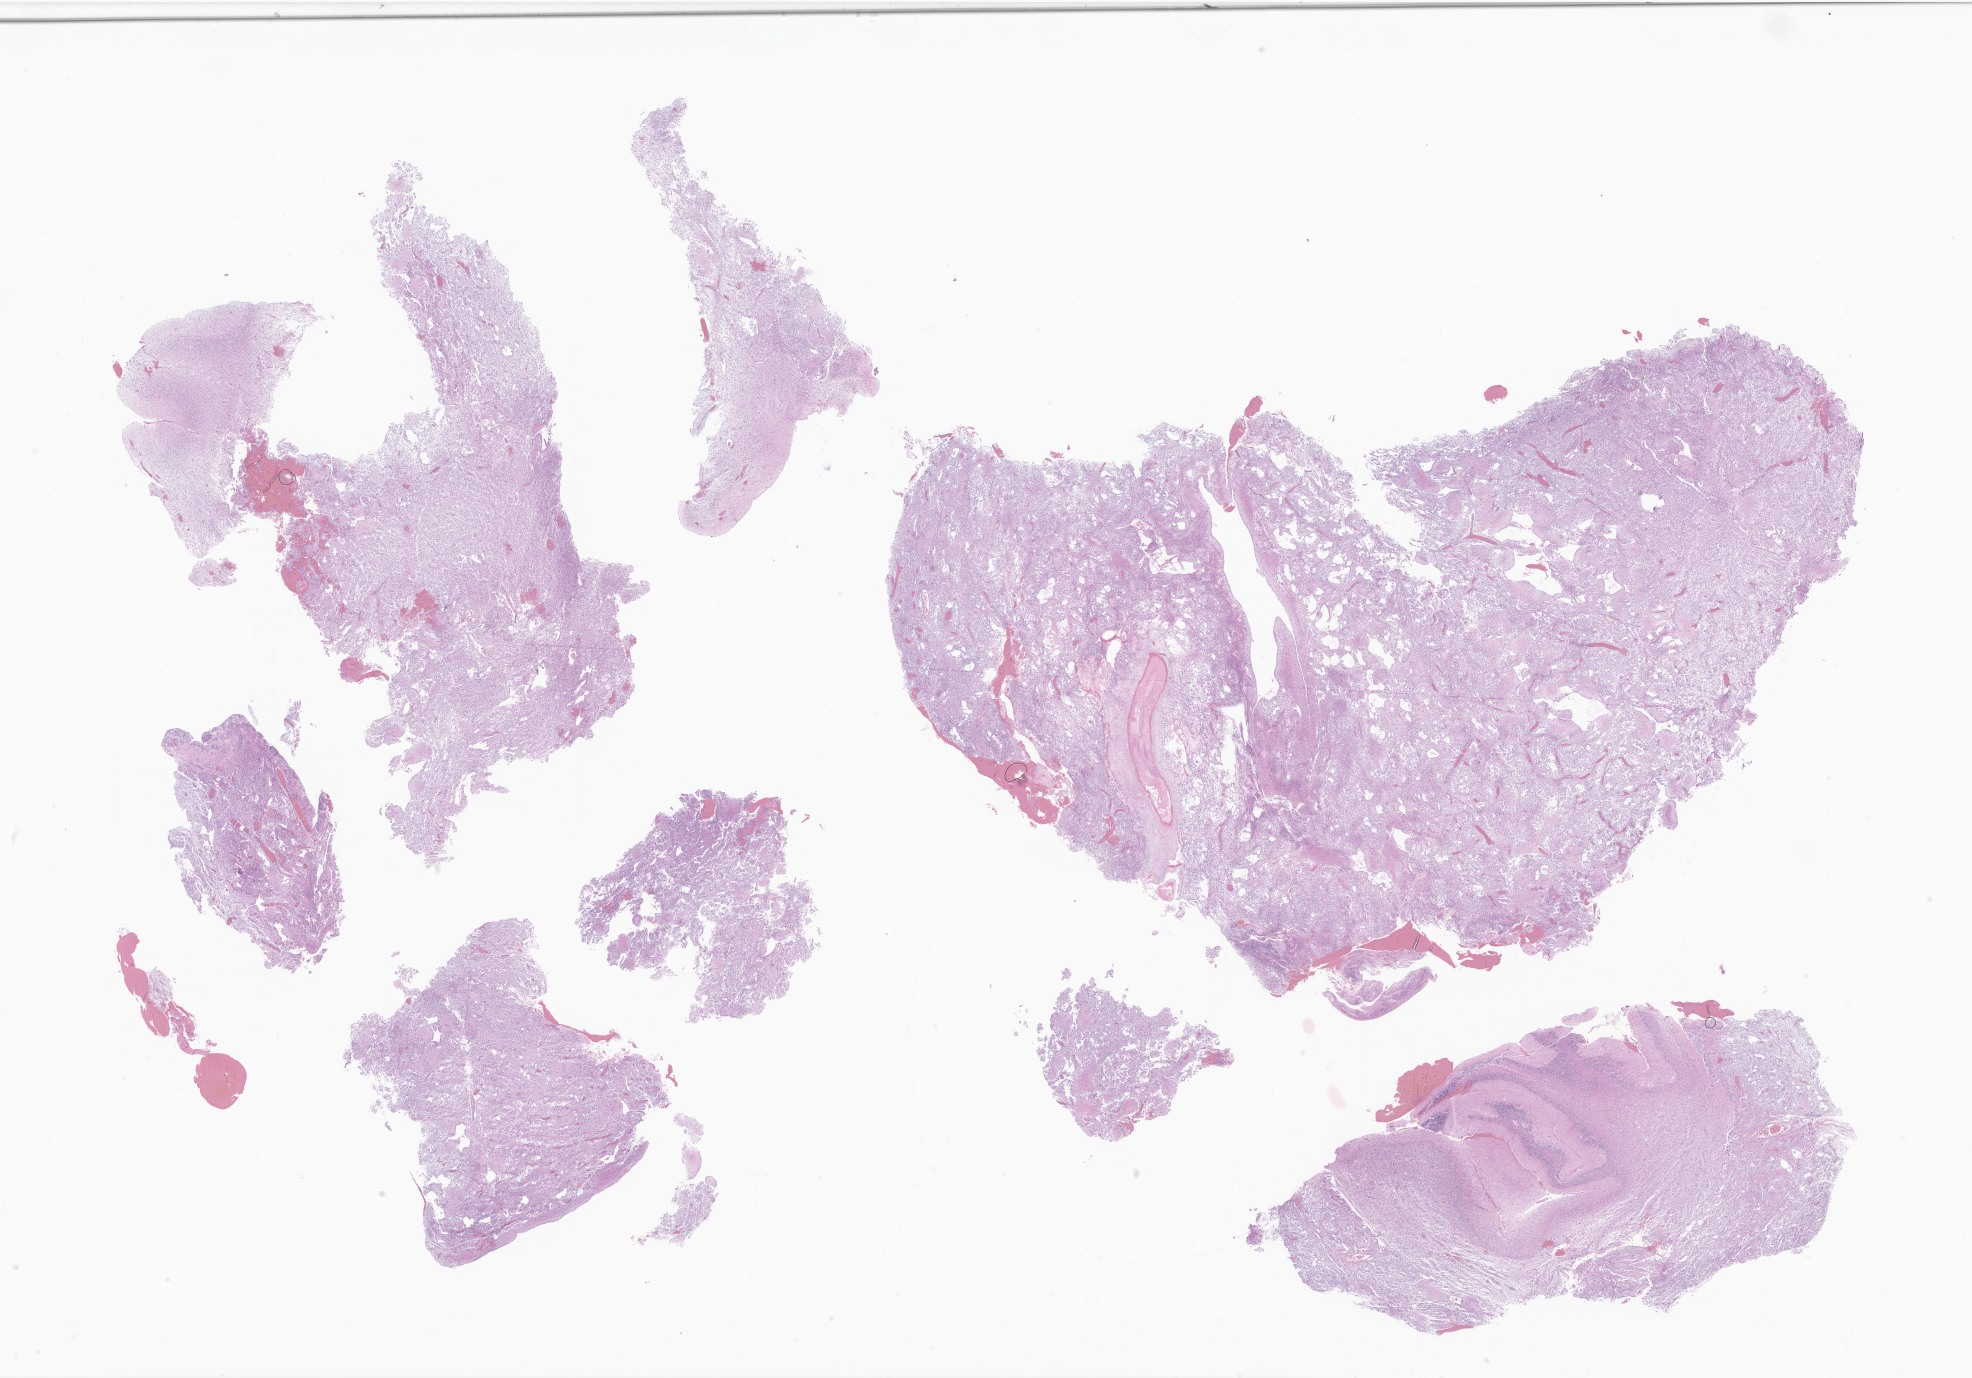
H&E whole-slide image of tumor tissue from the brain — a low-resolution overview of the entire scanned area, about 33.3 x 23.2 mm, formalin-fixed, paraffin-embedded (FFPE) tissue. Patient male; age 90 months (7 years 6 months).
Diagnosis (ICD-O-3 morphology term): Pilocytic astrocytoma.